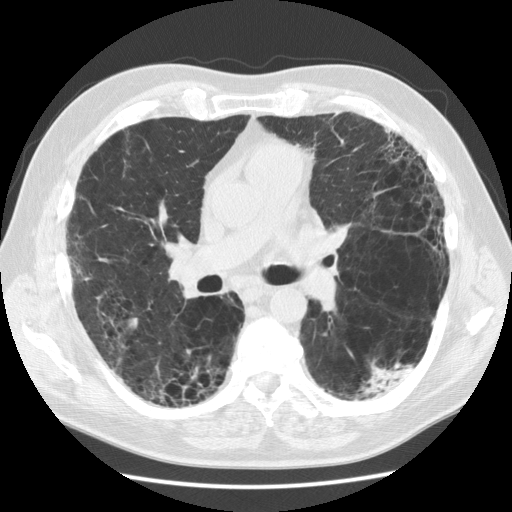
Low-dose screening chest CT, one axial slice; position 70 of 128 along the scan axis; reconstruction kernel STANDARD; lung window (W 1500 / L -600 HU); 512 × 512 image matrix, field of view 360 × 360 mm.
Outlined on this slice (manually delineated by an expert):
- lesion 1 (tumor, lower lobe of left lung): box from (x=366, y=365) to (x=410, y=390) px